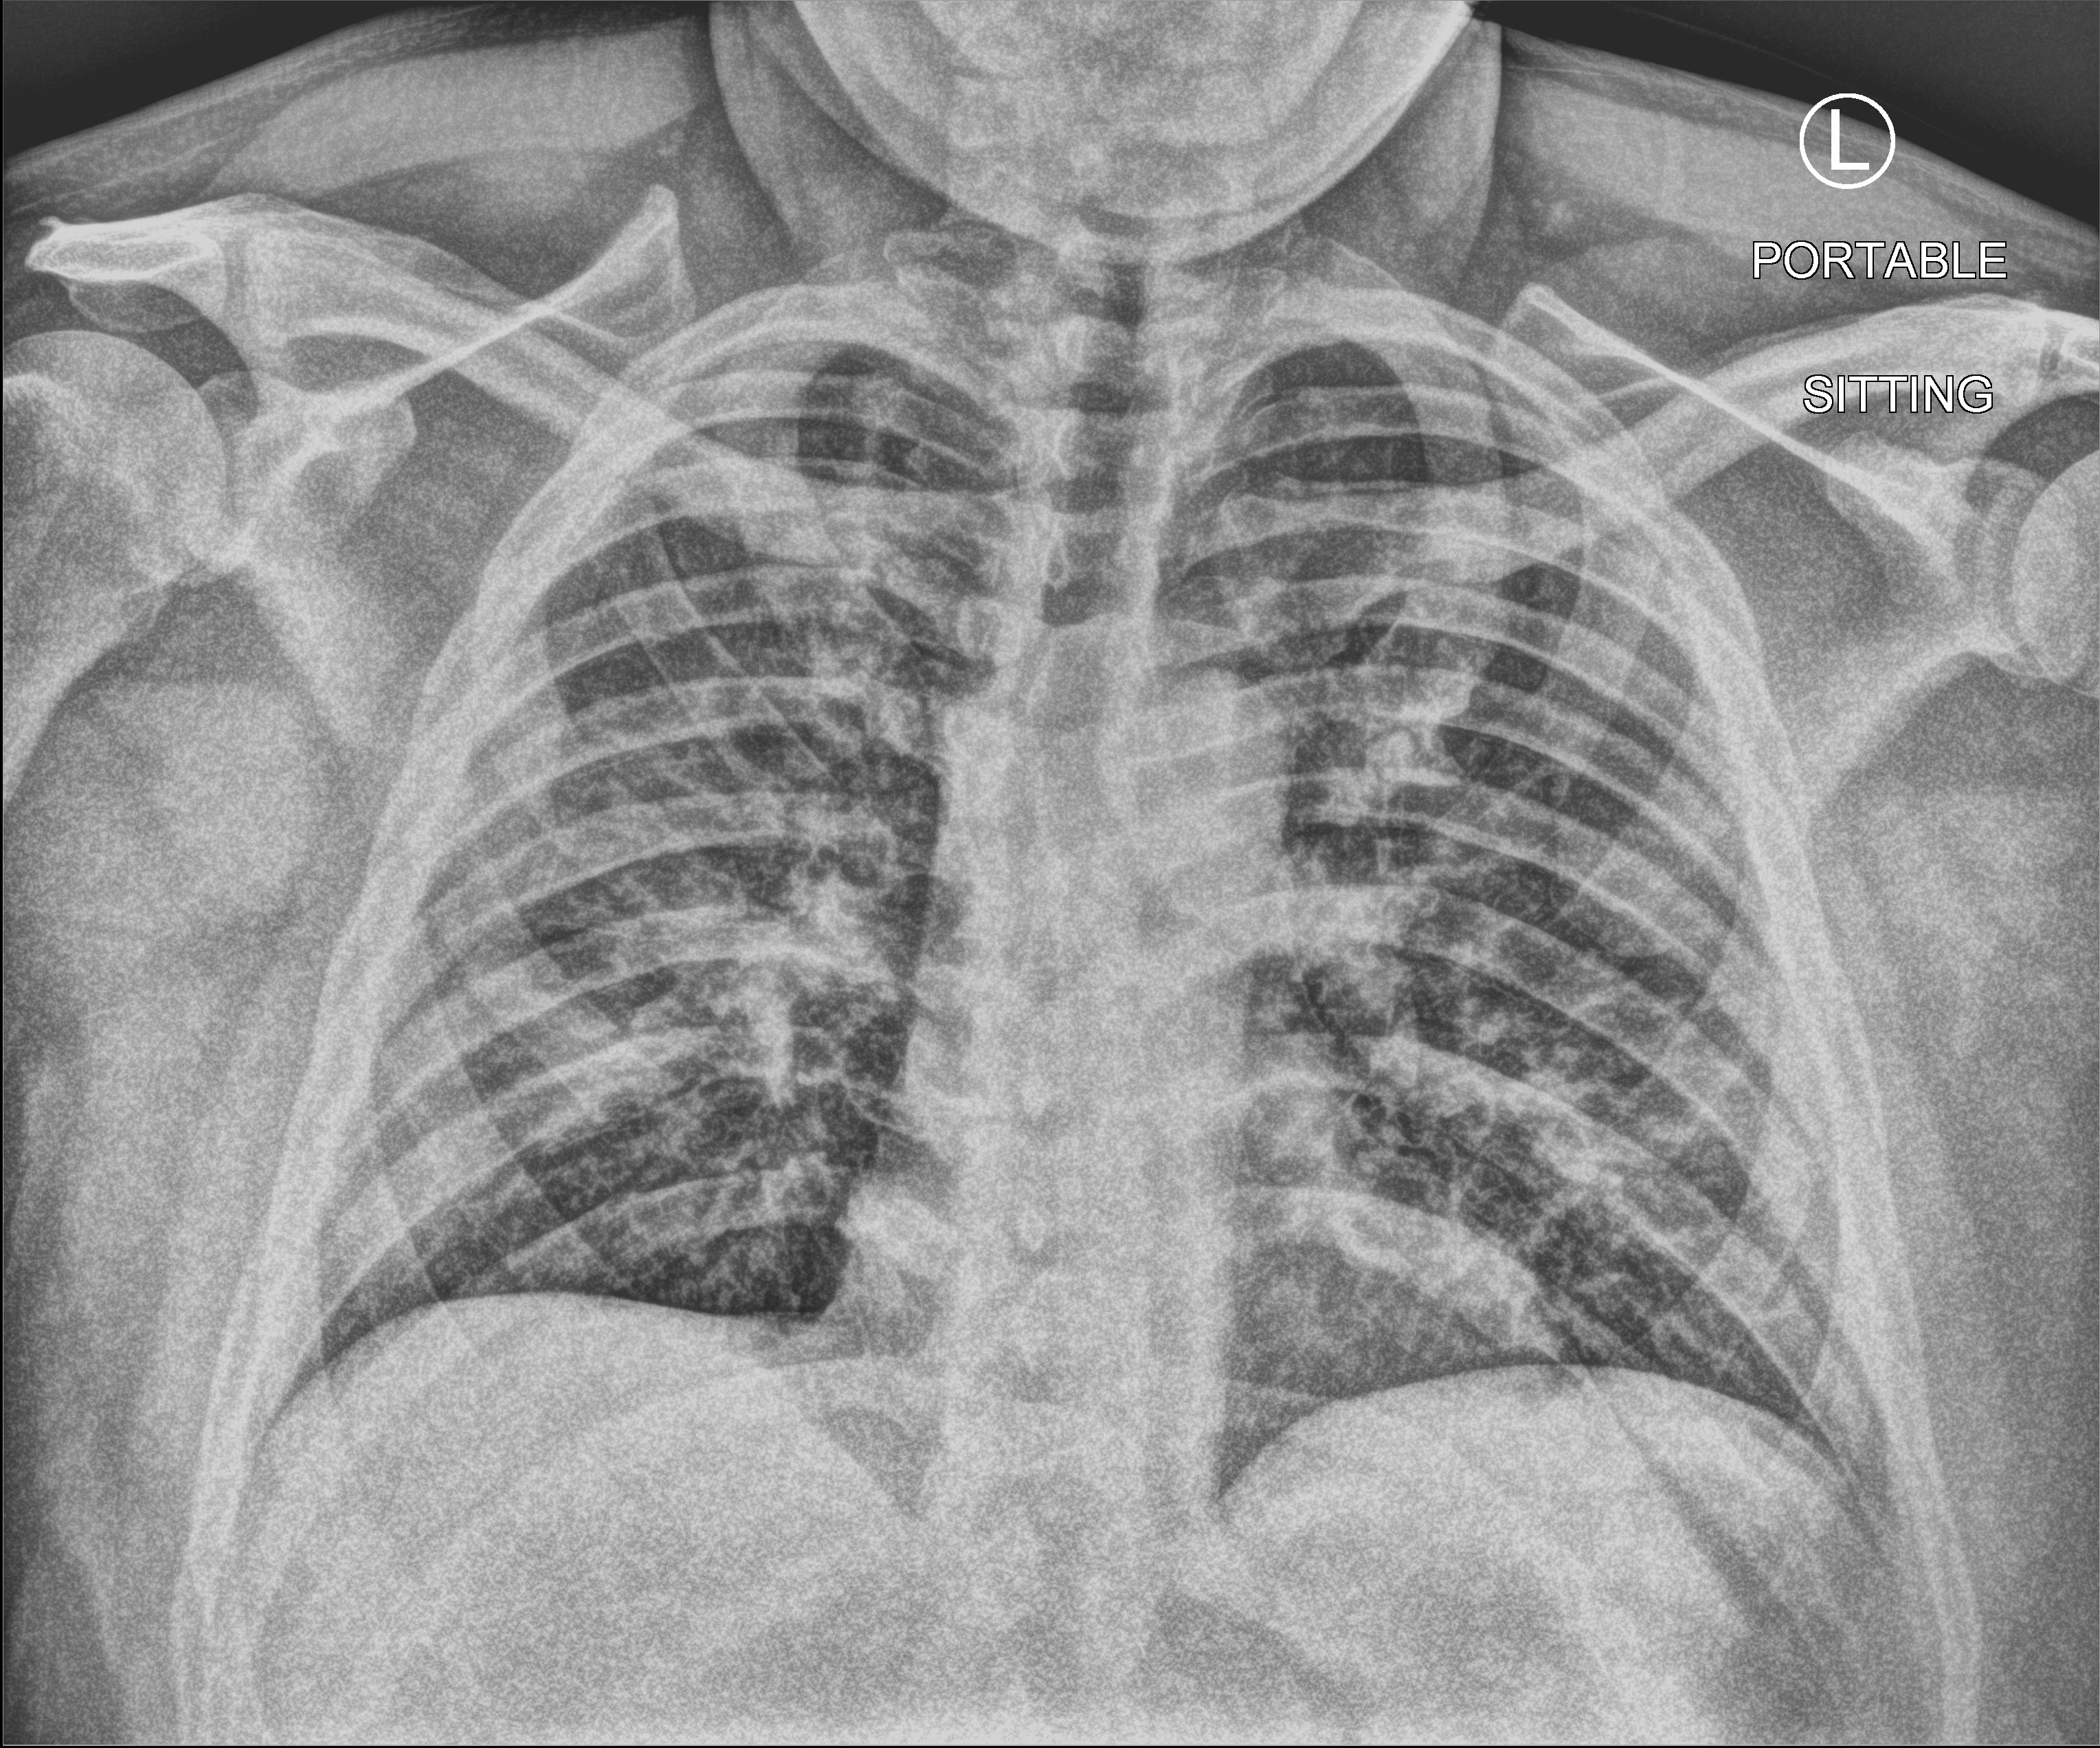
Portable chest radiograph; anteroposterior (AP) projection. Patient hospitalised with COVID-19; male, aged 18–59 years.
Hospital-stay facts (about this admission, not read from this image; timing relative to this image not recorded):
- mechanically ventilated during this hospital stay: no
- admitted to intensive care during this hospital stay: no
- length of hospital stay: 1 day